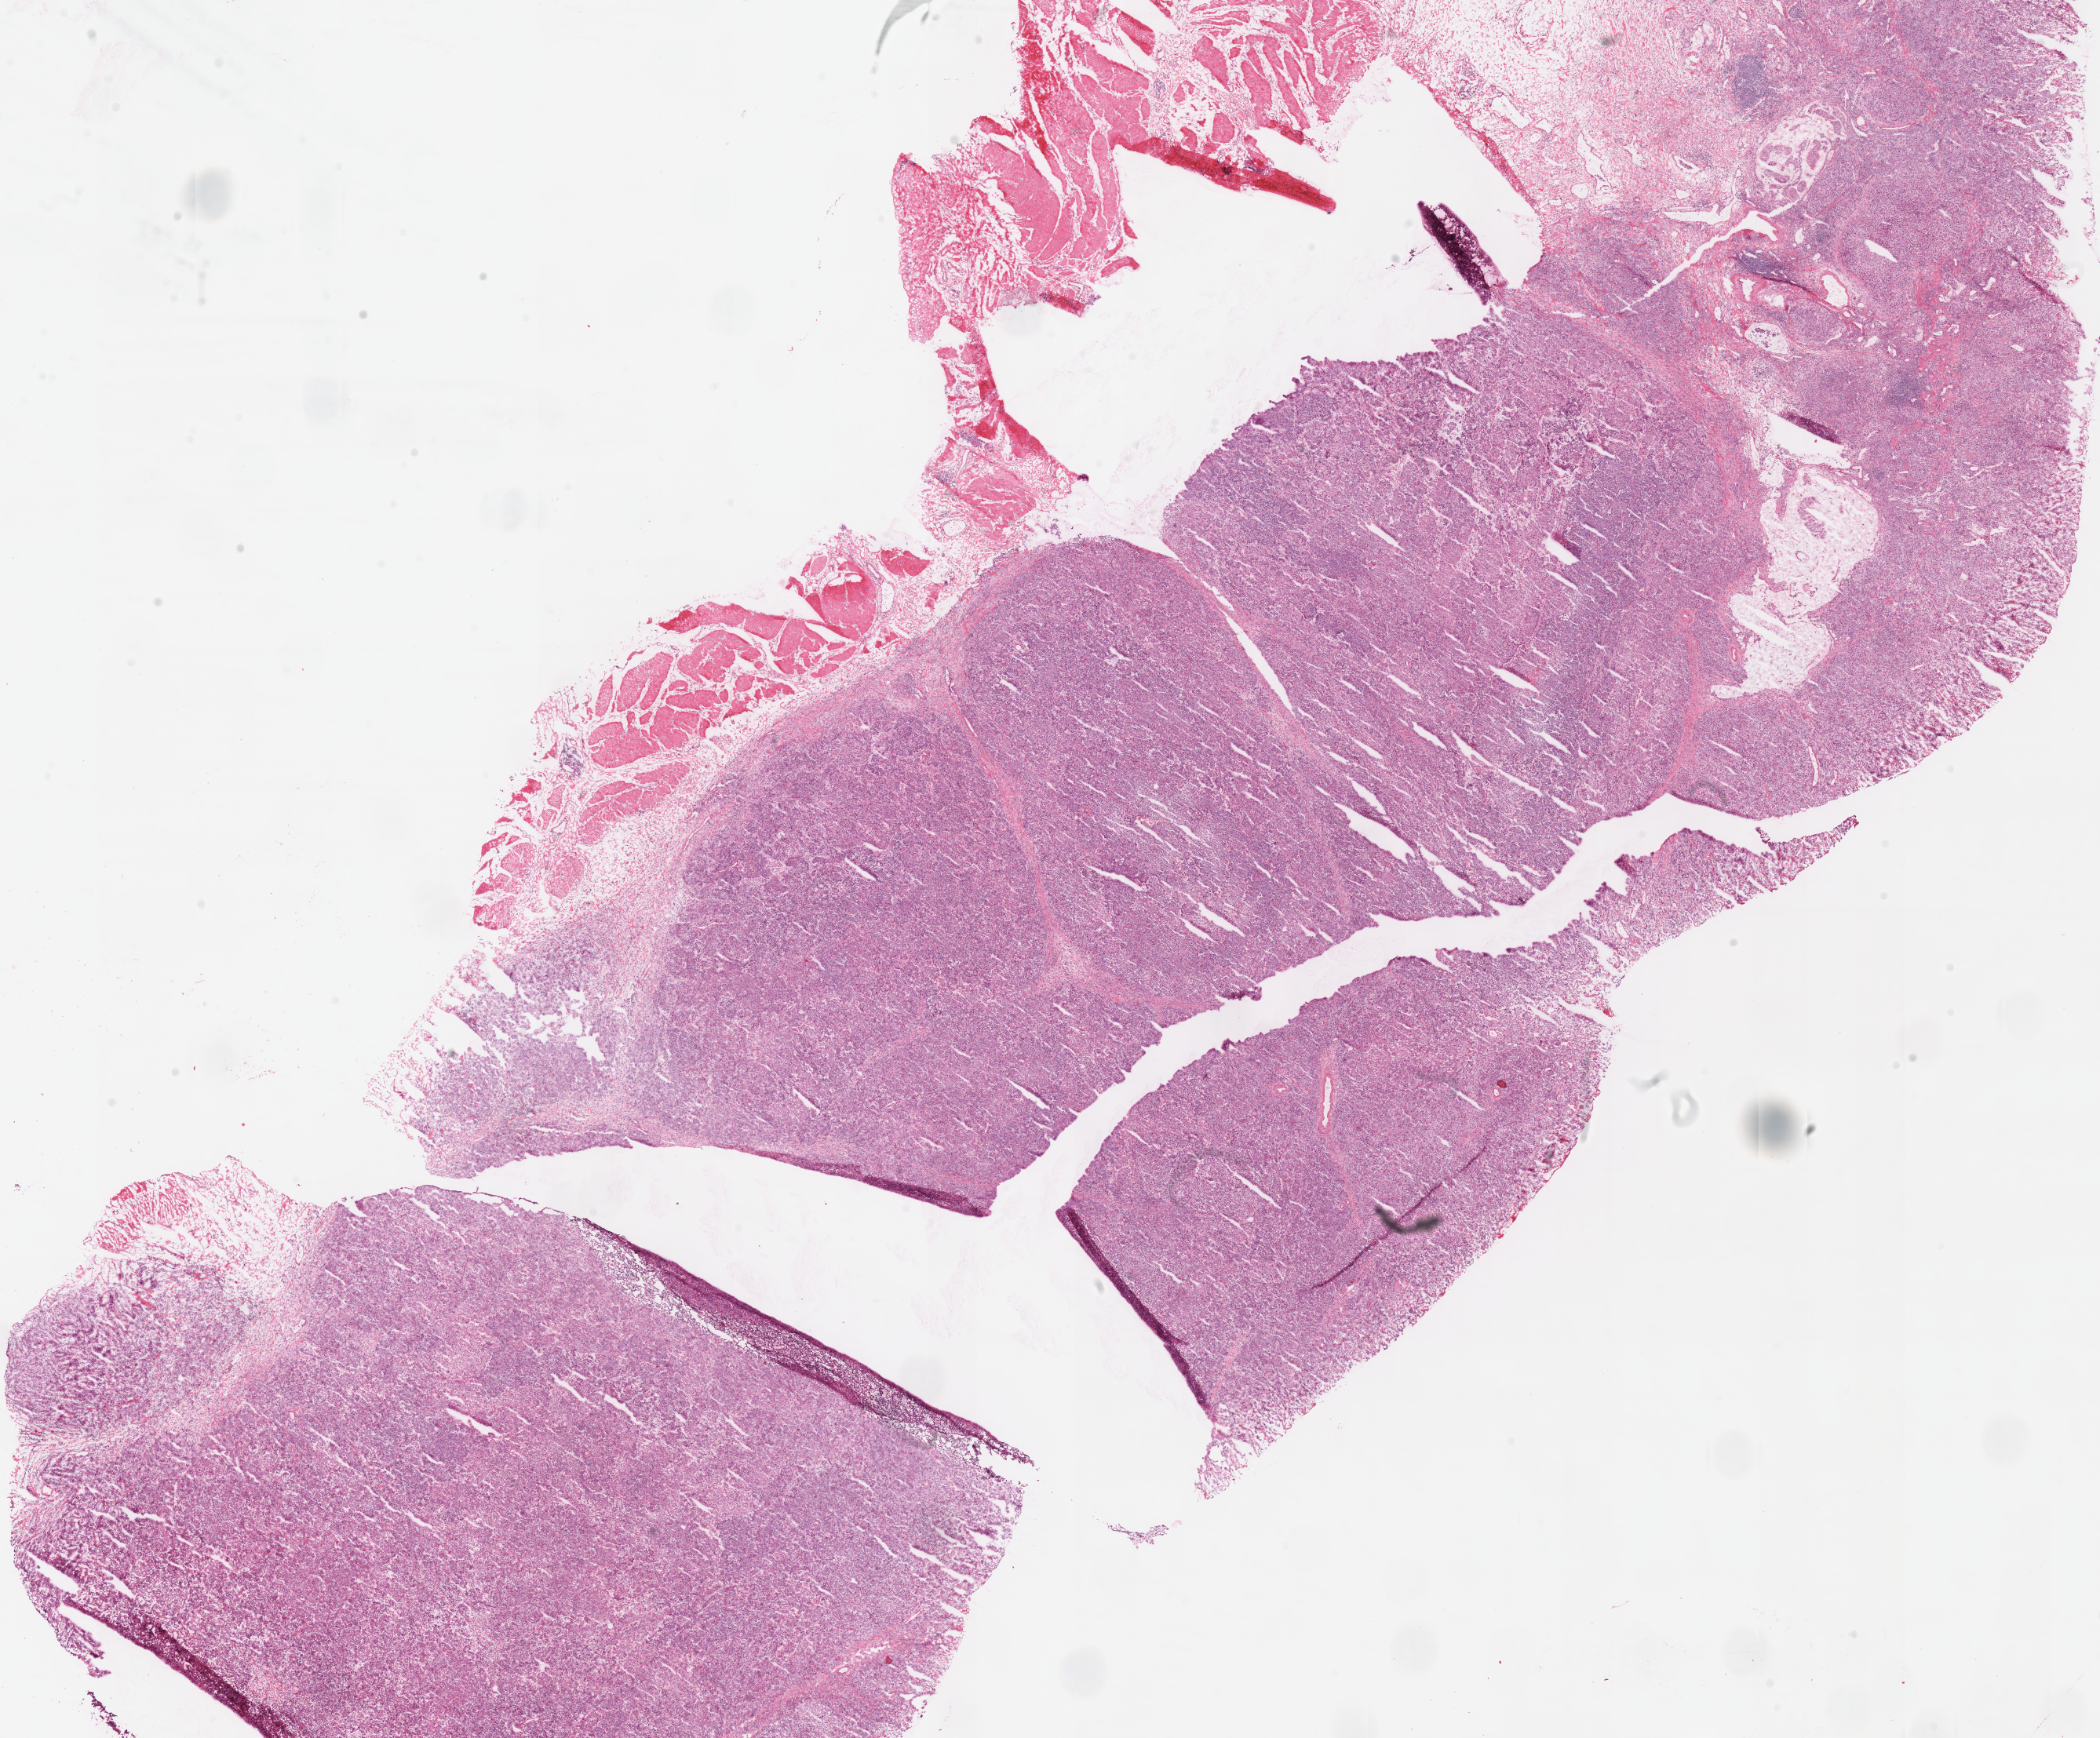
Digitized Hematoxylin and eosin (H&E) stained tissue section (whole slide) — whole scanned area (about 21.0 x 17.4 mm, slide scanned at 40x) shown as a low-resolution overview, frozen section from the top of the tissue portion, stomach, primary tumour sample. Female patient; age at initial diagnosis 84 years. Slide review estimates, as recorded: tumour cells 88%, tumour nuclei 75%.
Pathologic diagnosis: Adenocarcinoma, NOS (fundus of stomach).